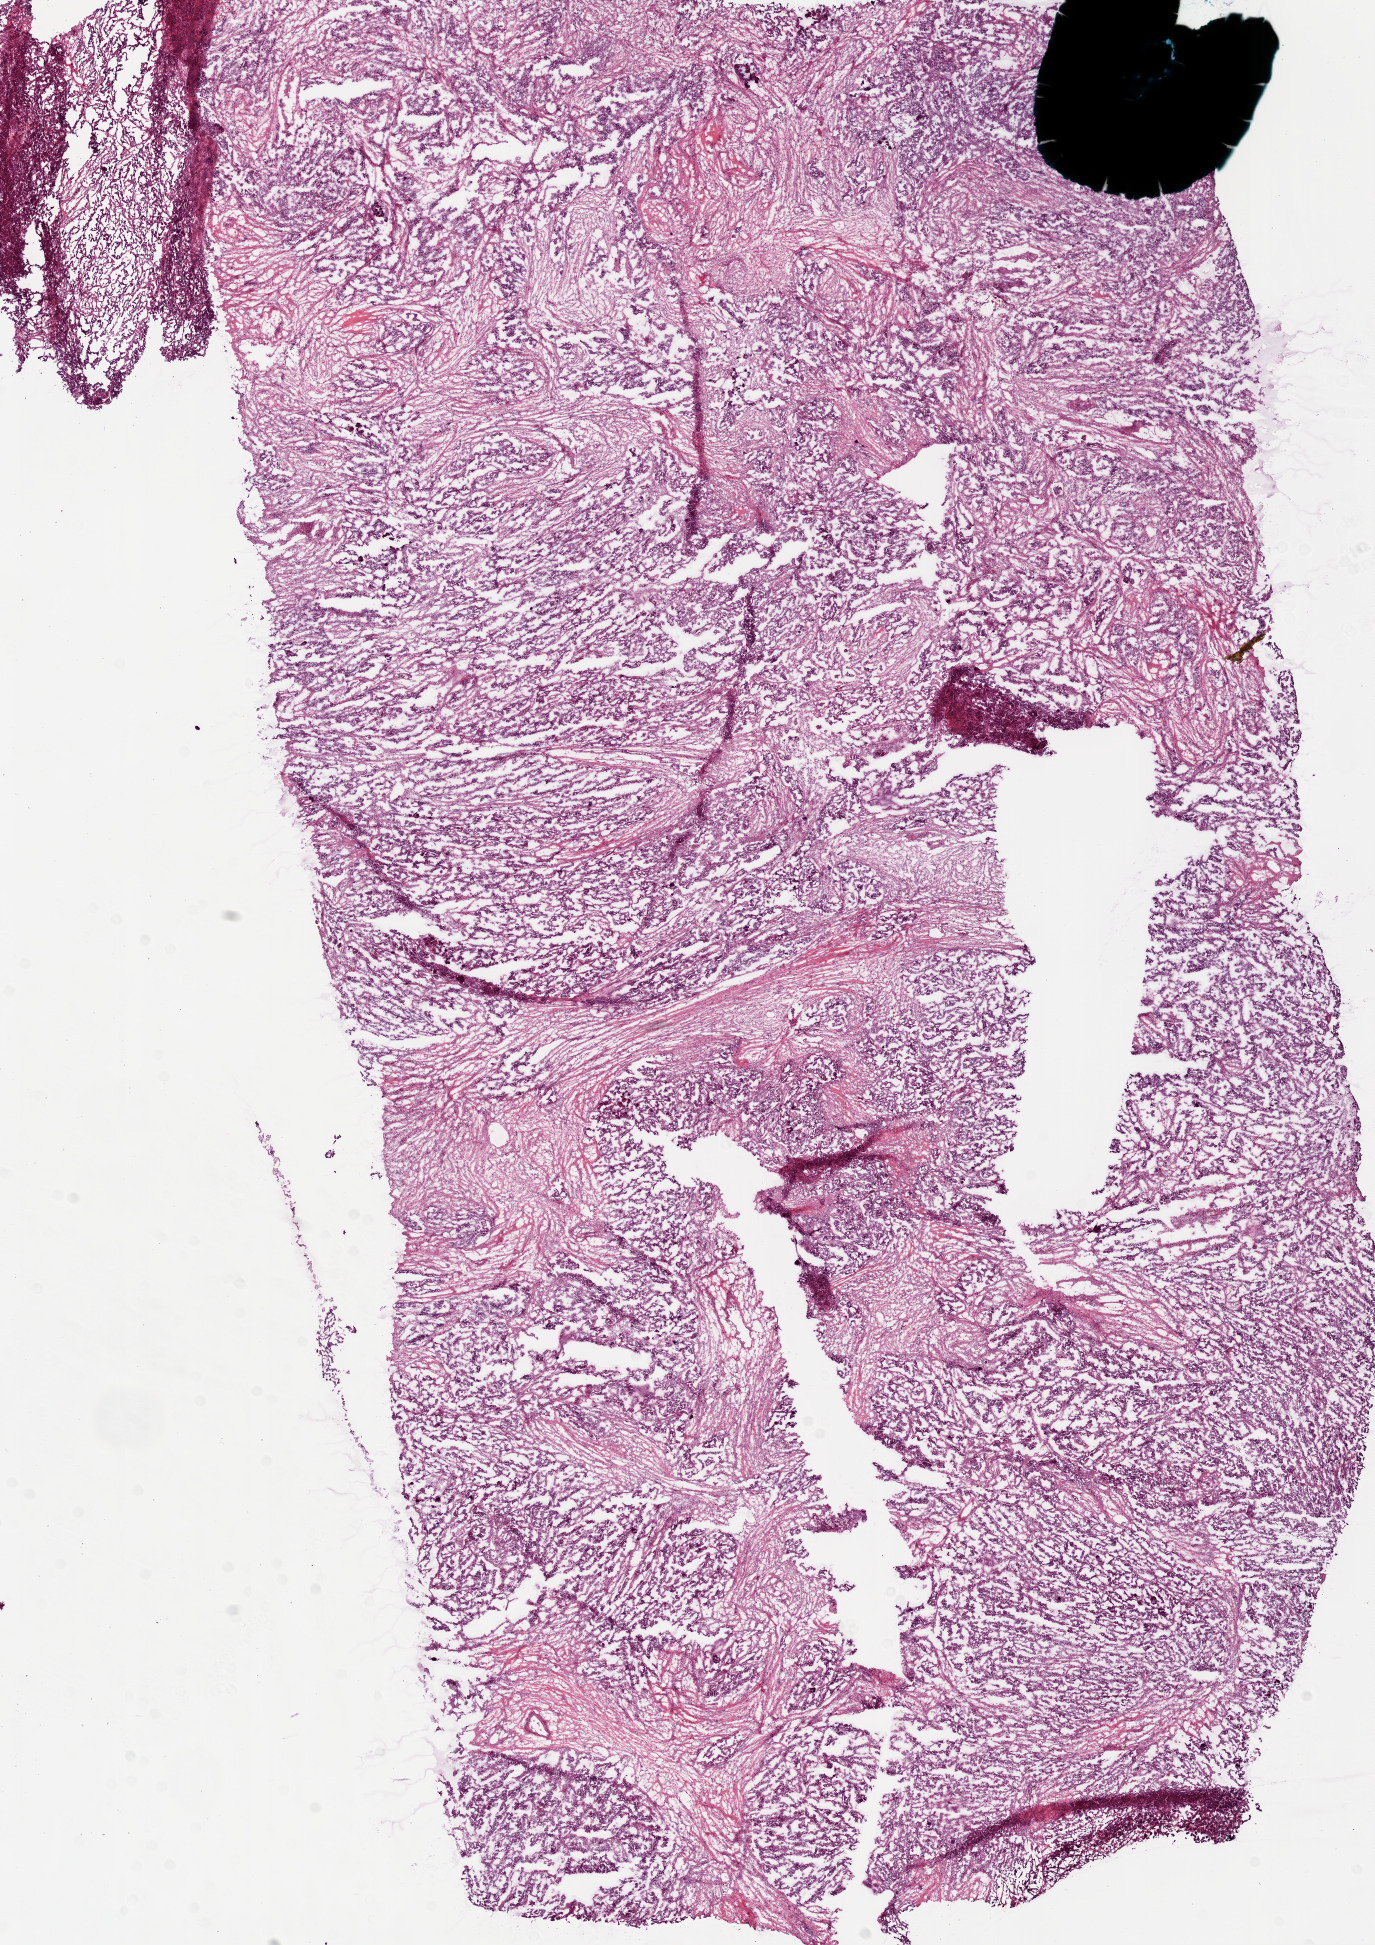
Hematoxylin and eosin (H&E) stained whole-slide image — shown as a low-resolution overview of the whole scanned area (about 11.0 x 15.6 mm, from a 20x scan), frozen section from the bottom of the tissue portion, ovary, primary tumour sample. Patient: female, age at initial diagnosis 41 years. Histologic grade: G3 (poorly differentiated). Composition of this section per pathologist review: tumour cells 89%, tumour nuclei 90%, normal cells 0%, stromal cells 10%, necrosis 1%.
Diagnosis: Serous cystadenocarcinoma, NOS. FIGO stage: IV.